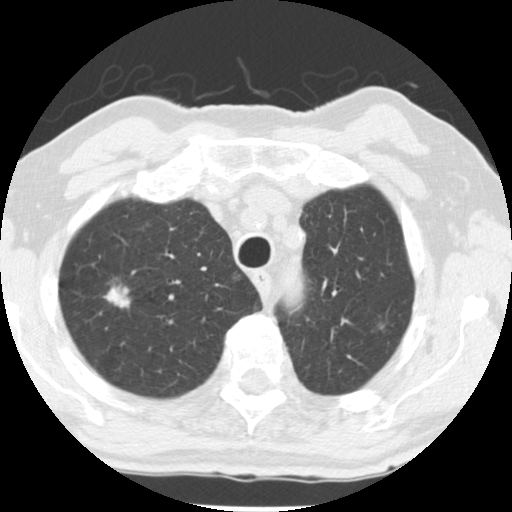
Low-dose screening chest CT, one axial slice; slice 206 of 252 in the series (ordered by position); 120 kVp; lung window (W 1500 / L -600 HU); 2.5 mm slice thickness; 512 × 512 image matrix.
Structures marked on this image (manually delineated by an expert):
- lesion 1 (tumor, upper lobe of right lung): bounding box (x1, y1, x2, y2) in pixels: (103, 284, 131, 308)